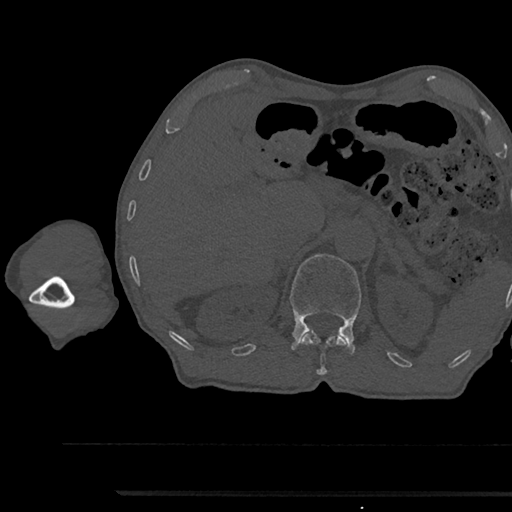
CT including the spine, one axial slice. Bone window (W 1800 / L 400 HU). 512 × 512 image matrix, field of view 367 × 367 mm. Patient: male, 79 years. Case-level facts recorded for this patient, not image findings: primary cancer: prostate.
Outlined on this slice (semi-automatic segmentation, software-assisted and operator-edited):
- L1 vertebra: box from (x=290, y=254) to (x=361, y=353) px
- T12 vertebra: (x=300, y=330)–(x=351, y=374)